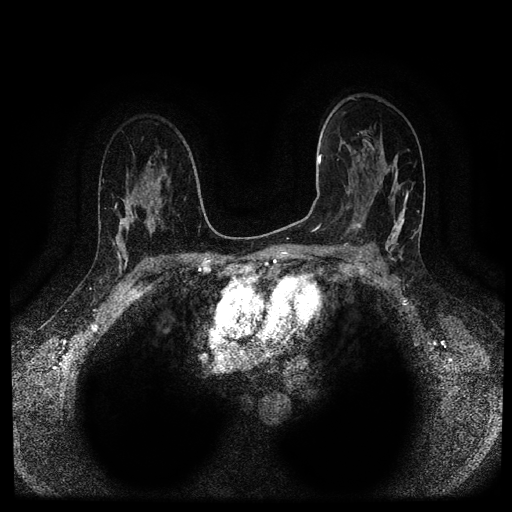
Breast MRI (dynamic contrast-enhanced, multi-phase), one axial slice; slice 66 of 116 in the series (ordered by position); dynamic contrast-enhanced series, time point 2 of 5 at this slice position (early post-contrast); 1.5 T; TE 2.6 ms, TR 5.3 ms; 512 × 512 image matrix, field of view 350 × 350 mm. Patient: female, 44 years.
Outlined on this slice (semi-automatic segmentation, software-assisted and operator-edited):
- breast lesion (labelled 'tumour' in the annotation; benign lesions carry a separate 'benign' label): bounding box [x1, y1, x2, y2] px = [352, 220, 364, 231]